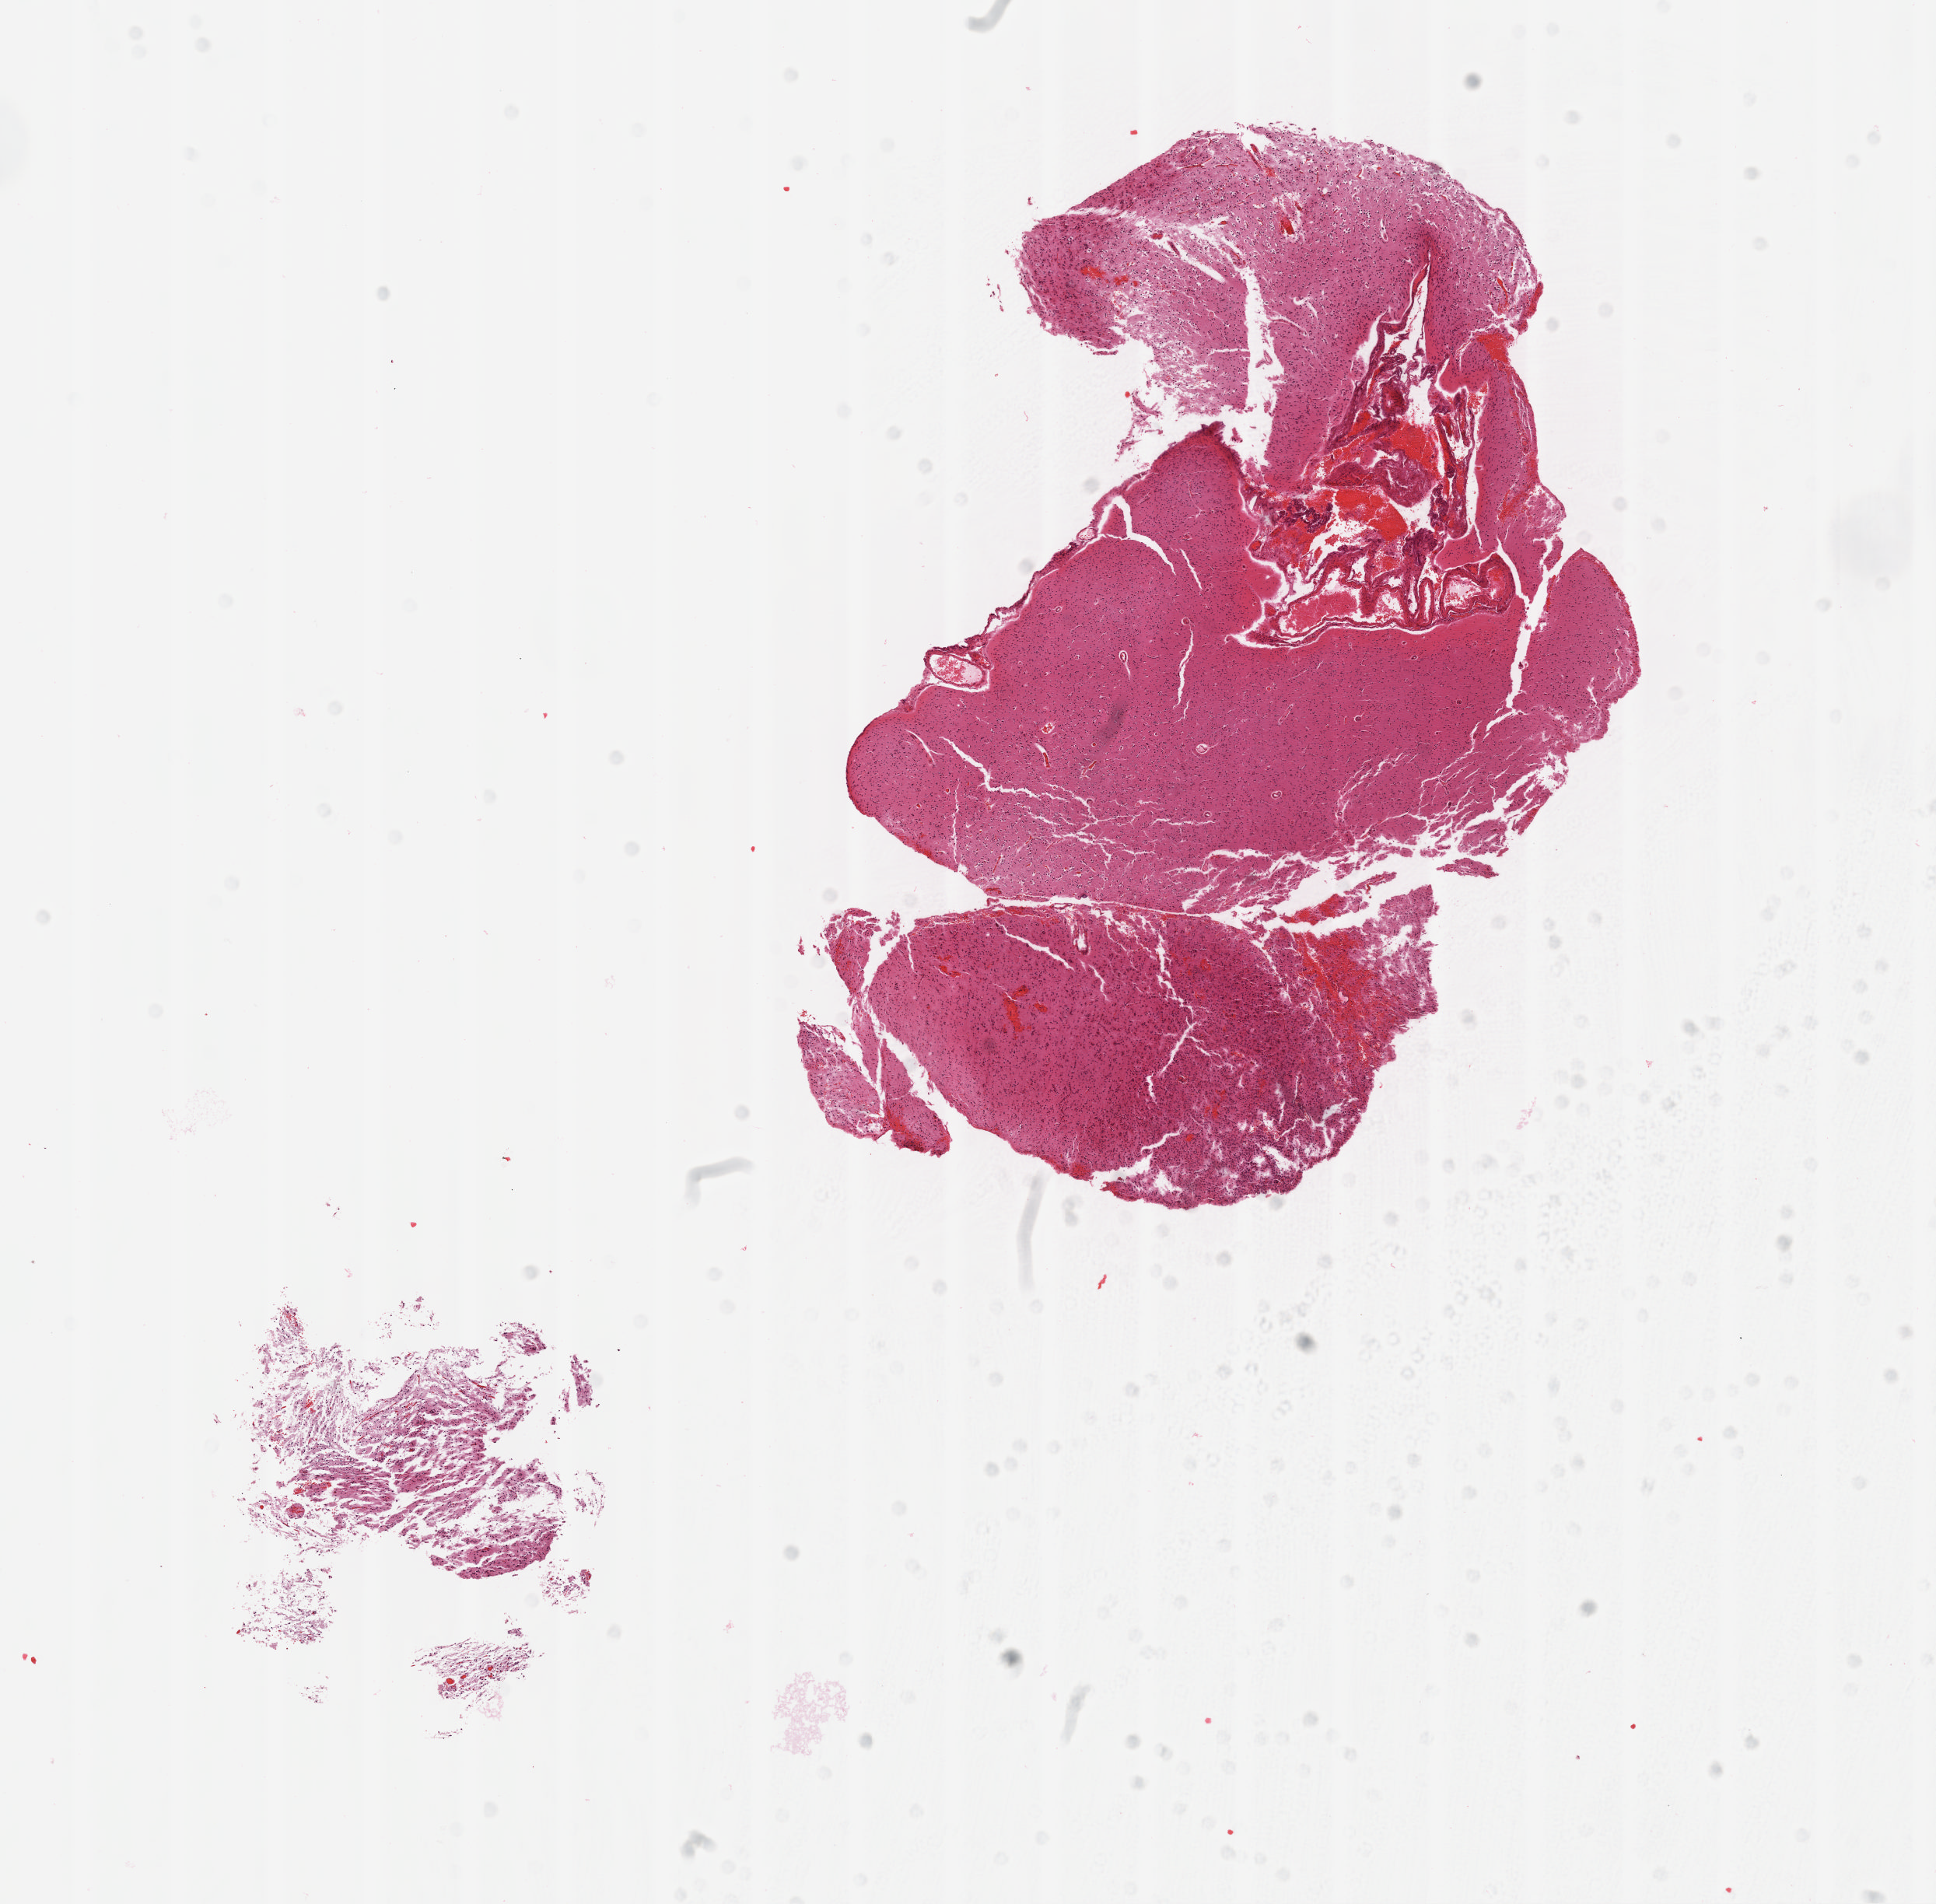
Digitized H&E tissue section (whole slide) — shown as a low-resolution overview of the whole scanned area (about 10.1 x 9.9 mm); FFPE section; sample: primary tumour, brain. Female, age 46 years at initial diagnosis. Histologic grade: G2 (moderately differentiated).
Histologic diagnosis: Oligodendroglioma, NOS.